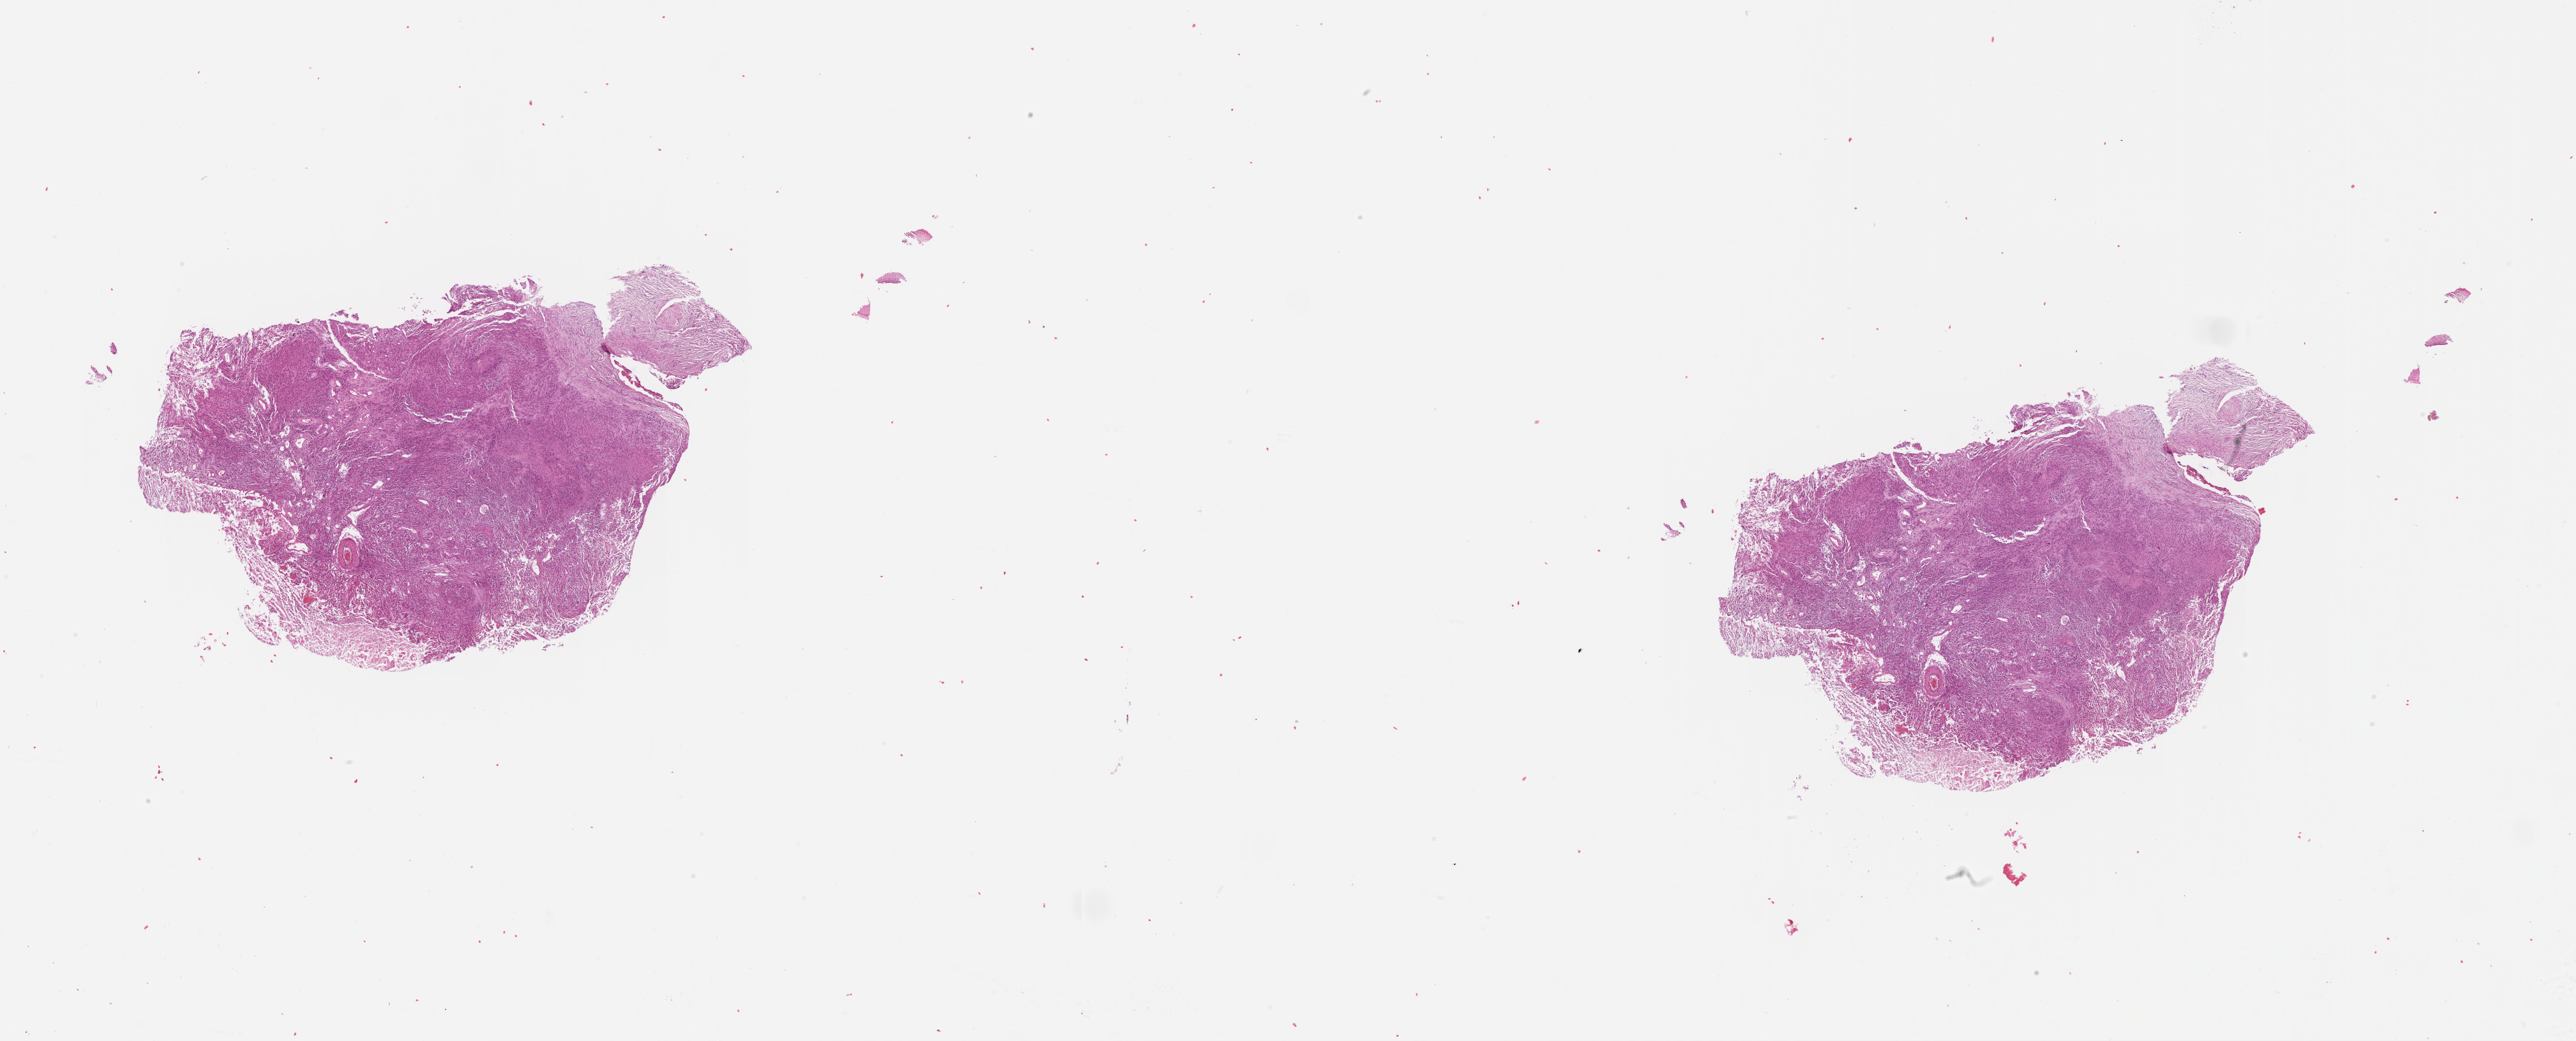
Whole-slide histology image, Hematoxylin and eosin (H&E) stained — low-resolution overview of the scanned area, about 31.1 x 12.6 mm (slide scanned at 20x). Tumour tissue sample, sampled site: brain. Male, 72 y/o. Slide review estimates, as recorded: tumour nuclei 75%, necrosis 10%.
Histologic diagnosis: Glioblastoma. Primary tumour site (as recorded): temporal lobe.